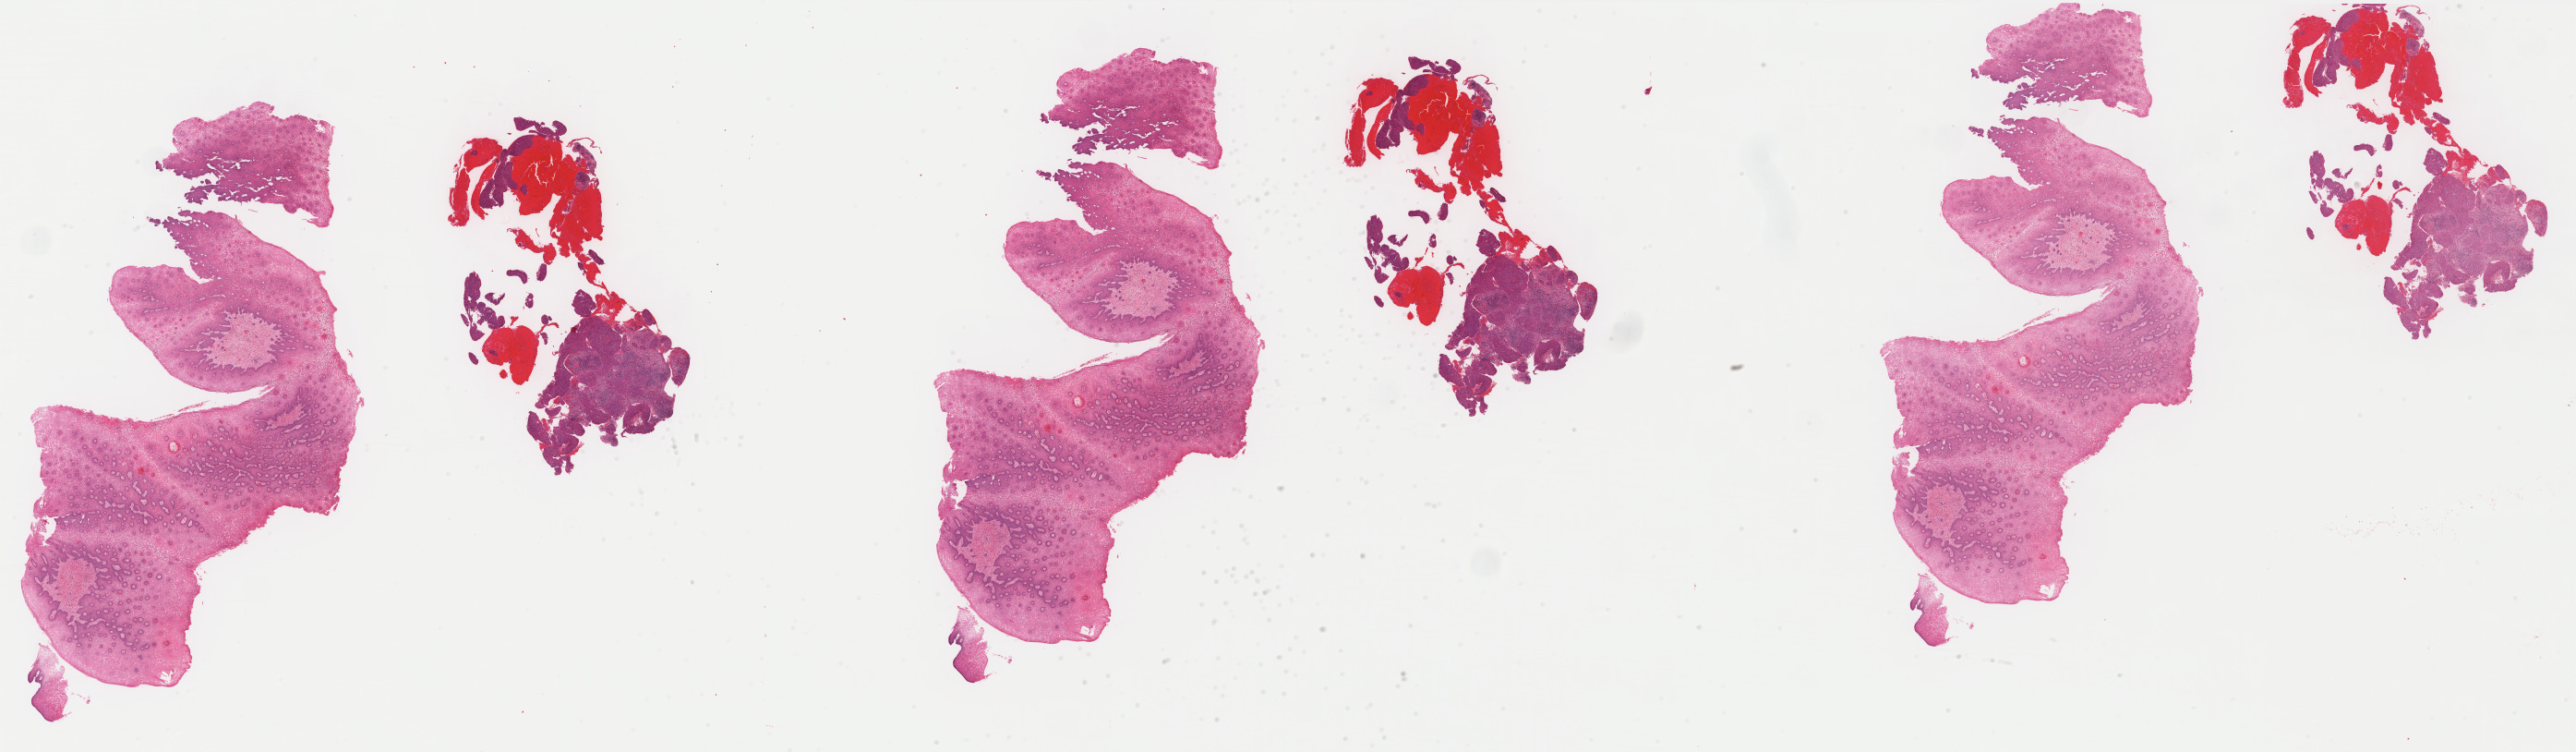
Hematoxylin and eosin (H&E) stained whole-slide image — a low-resolution overview of the entire scanned area, about 44.7 x 13.0 mm (from a 40x scan), formalin-fixed paraffin-embedded (FFPE) diagnostic section, cervix, primary tumour sample. Female, age 34 years at initial diagnosis. Histologic grade: G2 (moderately differentiated).
* histologic diagnosis: Squamous cell carcinoma, NOS (cervix uteri)
* FIGO stage: IIB